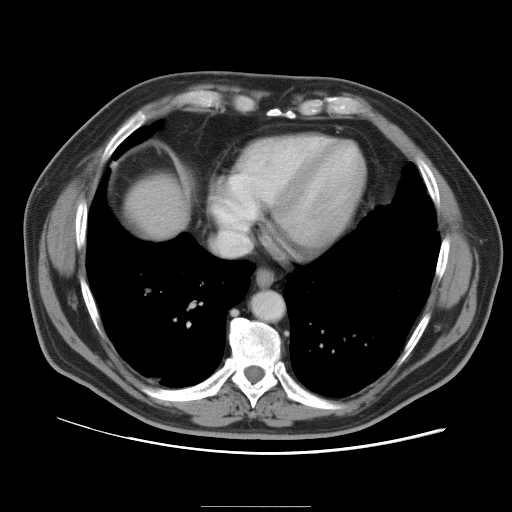
Contrast-enhanced abdominal CT, one axial slice. Position 95 of 105 along the scan axis. 120 kVp. Intravenous contrast given. Soft-tissue window (W 400 / L 40 HU). 5 mm slice thickness. 512 × 512 image matrix, field of view 399 × 399 mm. Male patient, age 64 years. From the clinical record (not read from this slice): diagnosis: colorectal cancer liver metastases, imaged before liver resection; multiple liver metastases: yes; largest metastasis: 3 cm.
Annotated regions visible in this slice (manually delineated by an expert):
- liver: box from (x=127, y=178) to (x=187, y=239) px
- planned liver remnant (the part of the liver to remain after resection): (x=128, y=178)–(x=187, y=239)